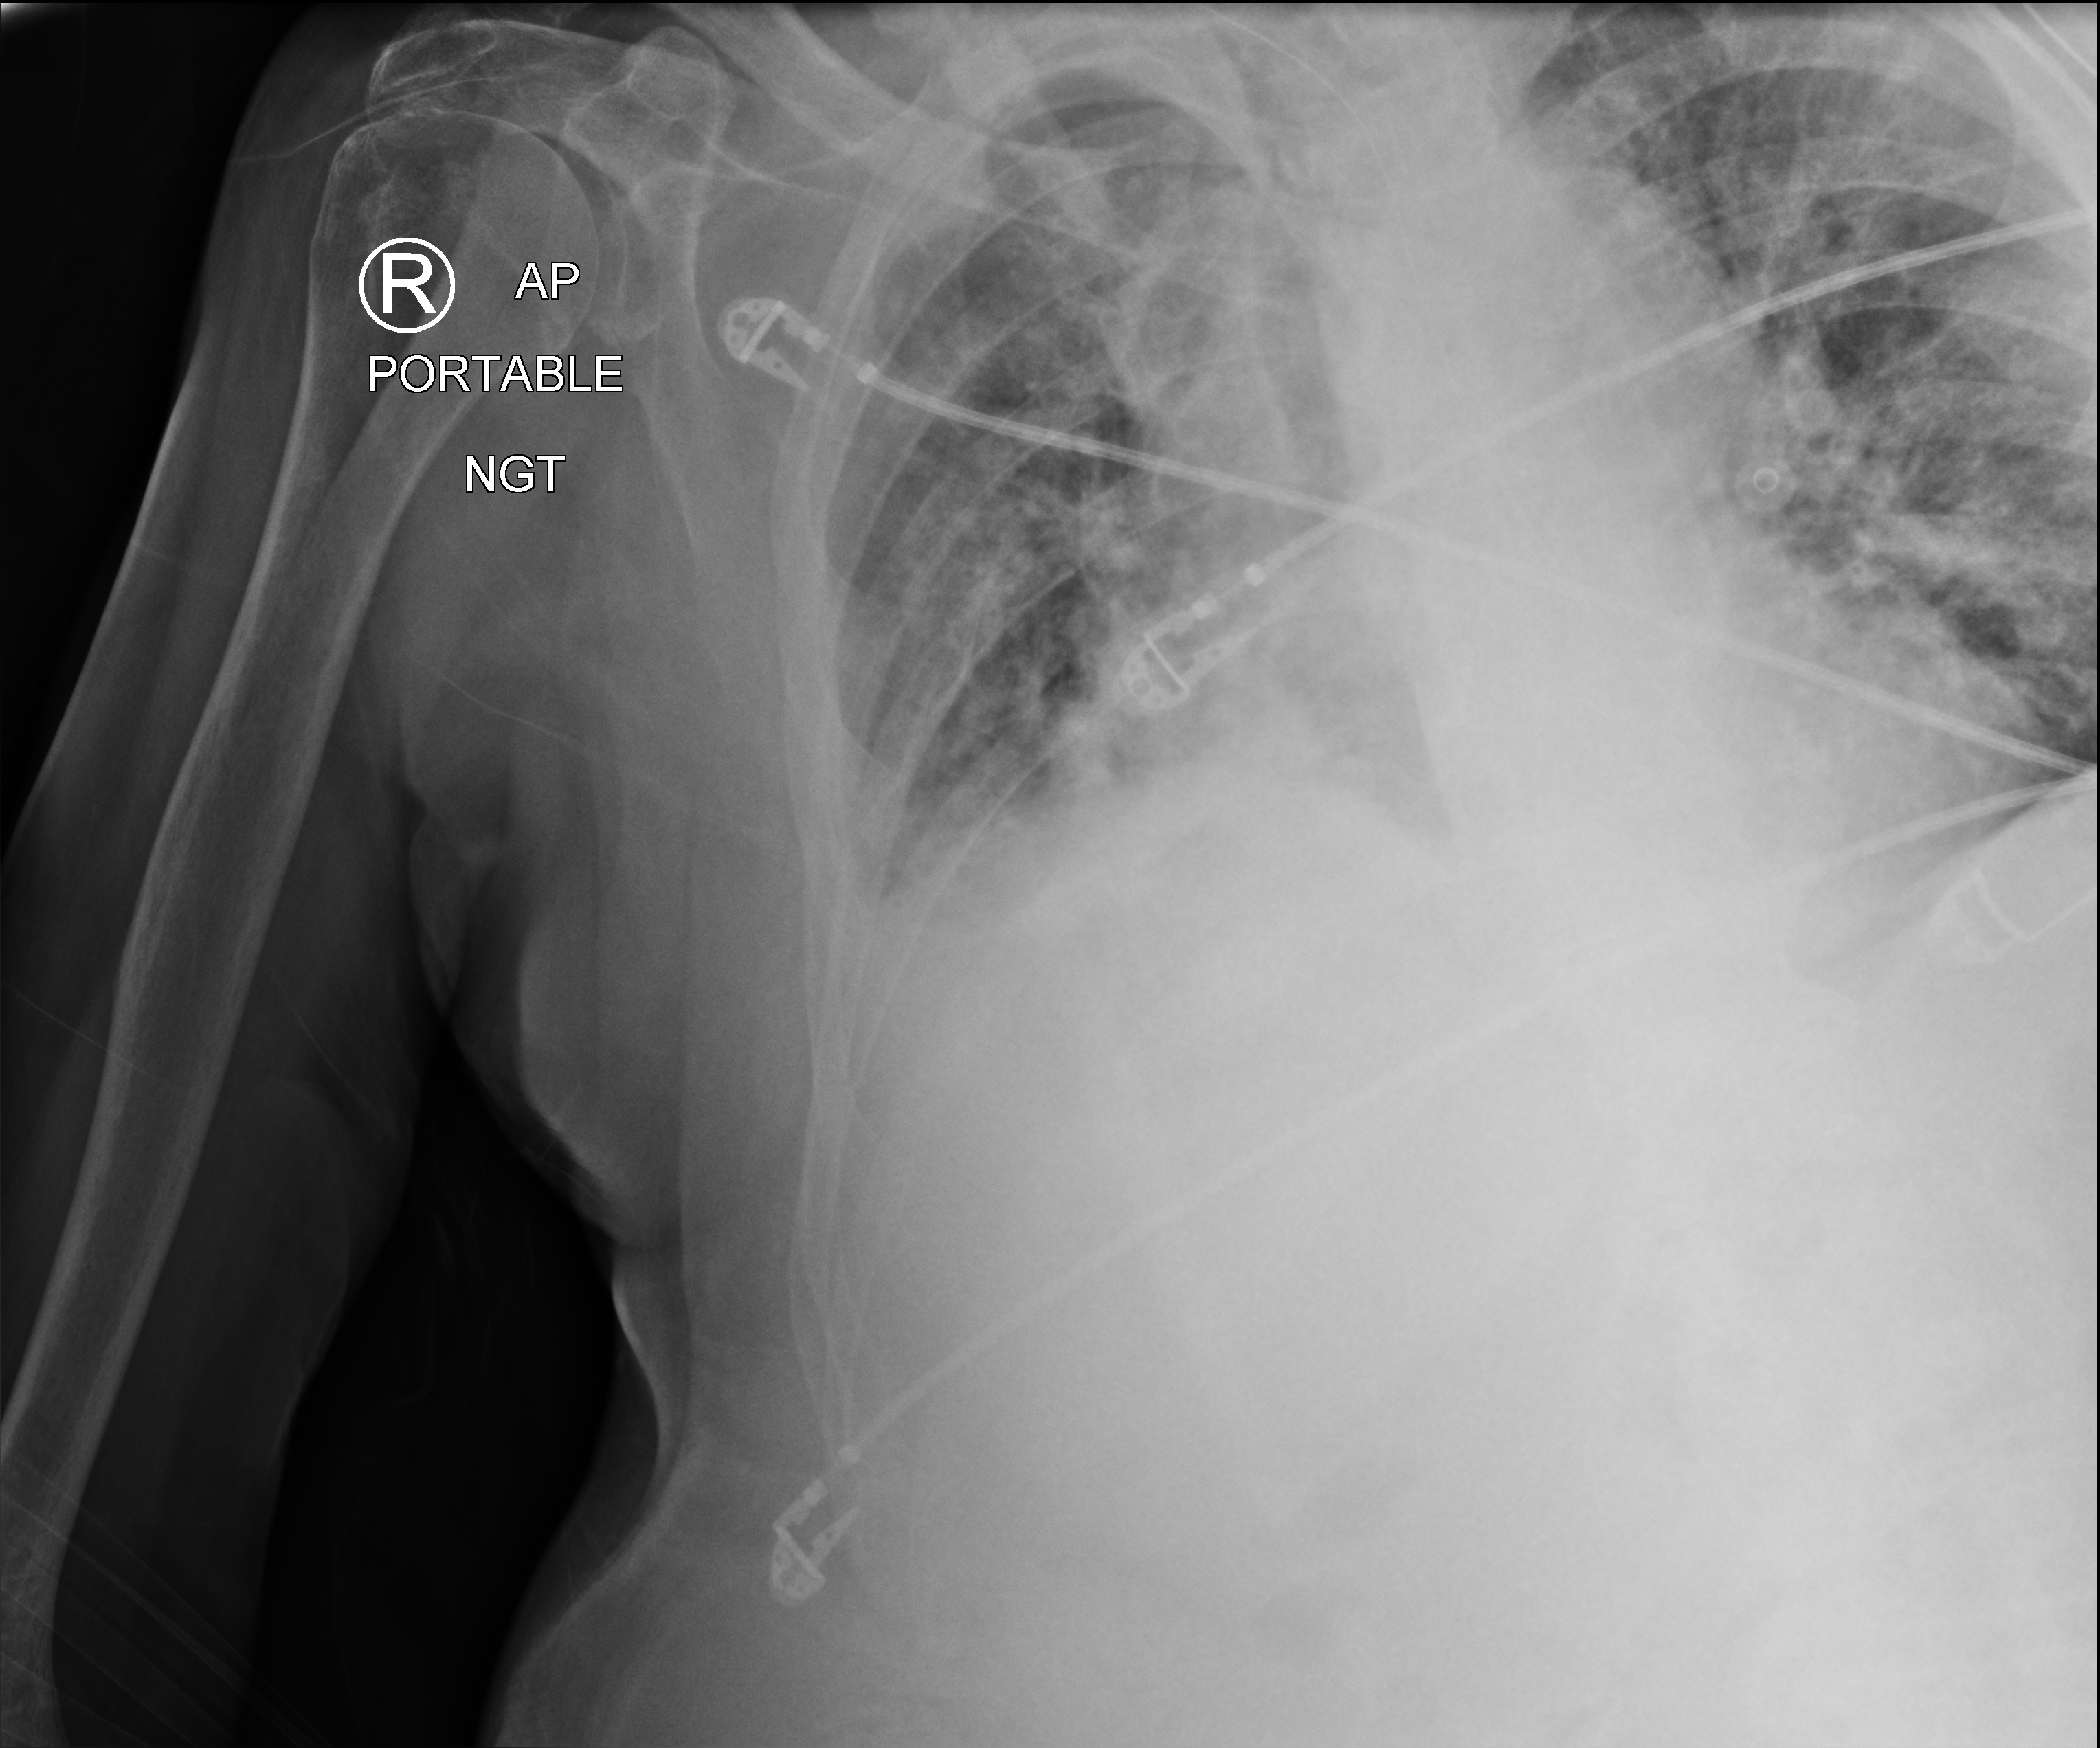
Chest X-ray (portable), anteroposterior (AP) projection. Male patient hospitalised with COVID-19, age 75–90 years.
From the hospital-stay record, not from the radiograph (when in the stay this image was taken is not recorded): length of hospital stay: 5 days; admitted to intensive care during this hospital stay: no; mechanically ventilated during this hospital stay: no.